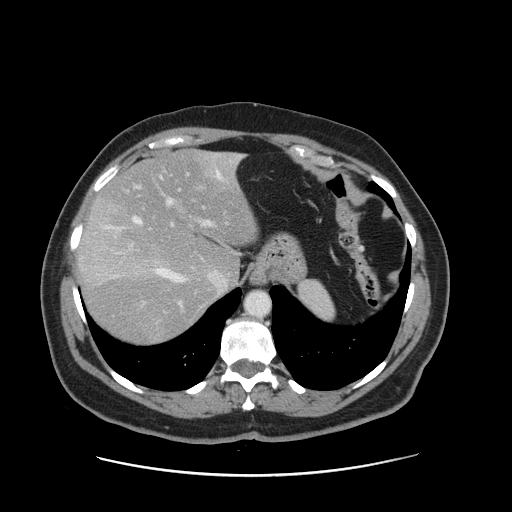
Contrast-enhanced abdominal CT, one axial slice; slice 116 of 161 in the series (ordered by position); intravenous contrast given; soft-tissue window (W 400 / L 40 HU); 2.5 mm slice thickness; 512 × 512 image matrix, field of view 398 × 398 mm. Female patient, age 62 years. From the clinical record (not read from this slice): diagnosis: colorectal cancer liver metastases, imaged before liver resection; multiple liver metastases: no; largest metastasis: 2.5 cm; disease in both lobes: no.
Outlined on this slice (expert manual segmentation):
- hepatic veins: box from (x=104, y=155) to (x=241, y=286) px
- liver: (x=77, y=150)–(x=259, y=346)
- planned liver remnant (the part of the liver to remain after resection): (x=96, y=150)–(x=258, y=283)
- portal vein (with intrahepatic branches): (x=162, y=170)–(x=214, y=305)